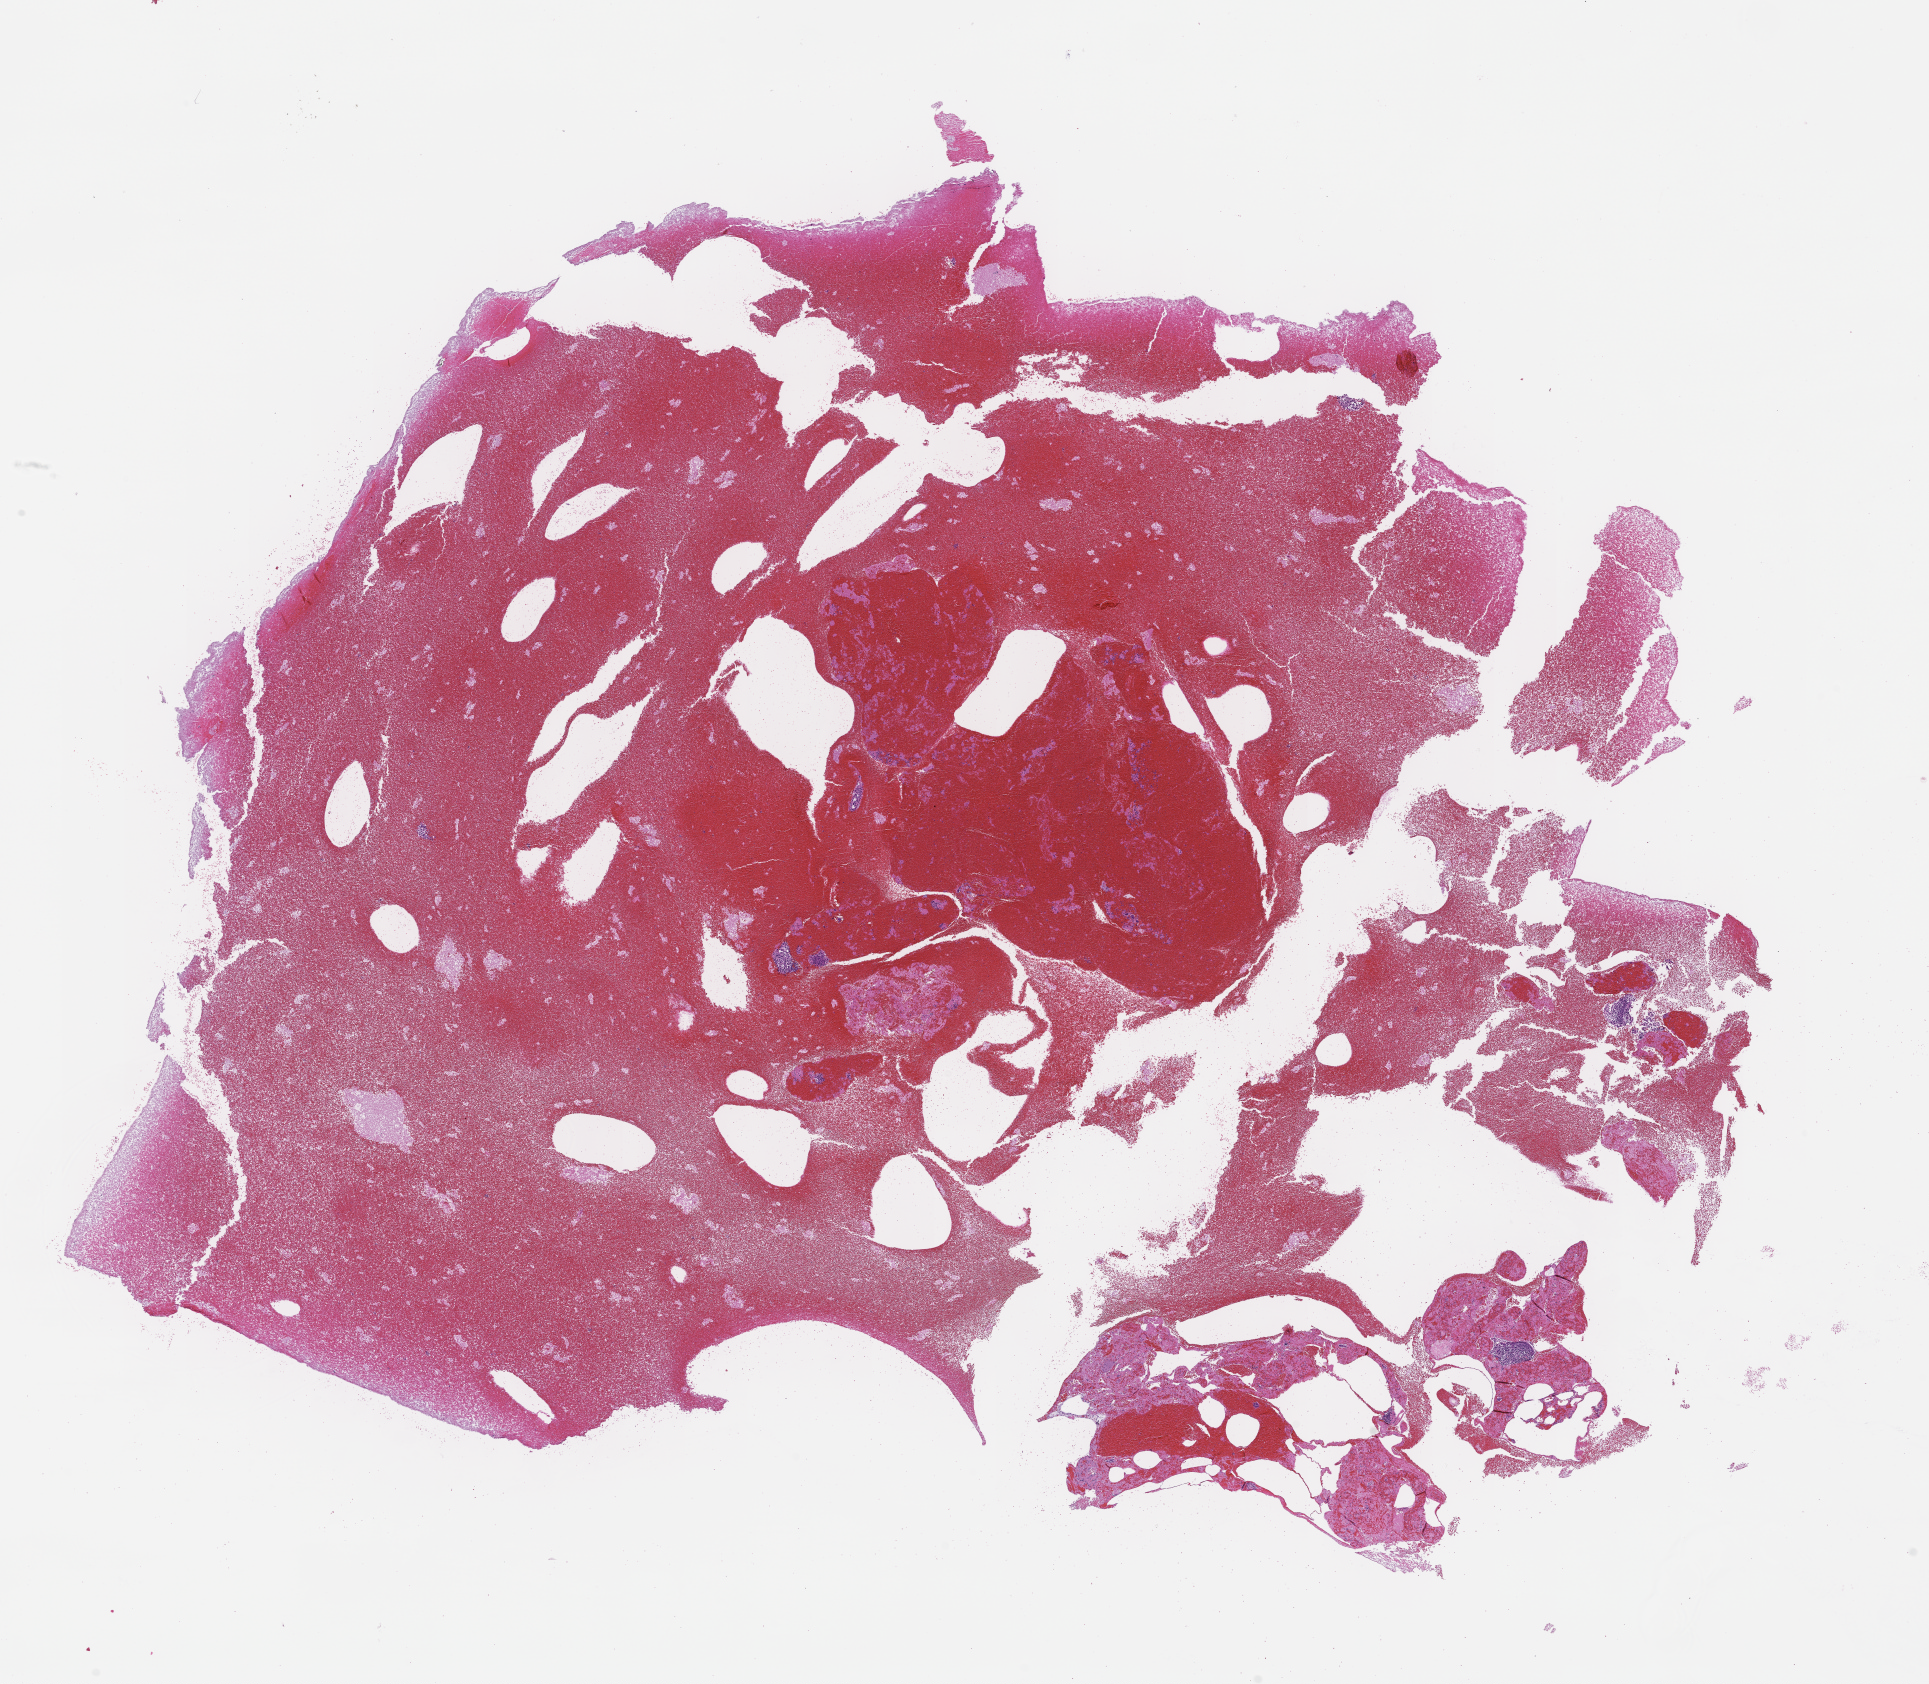
Hematoxylin and eosin (H&E) whole-slide image — low-resolution overview of the scanned area, about 15.6 x 13.6 mm, formalin-fixed paraffin-embedded section, specimen time point: archival tissue. Patient: male.
- this section: metastatic tumor tissue
- patient diagnosis (primary): Non-Small Cell Lung Carcinoma